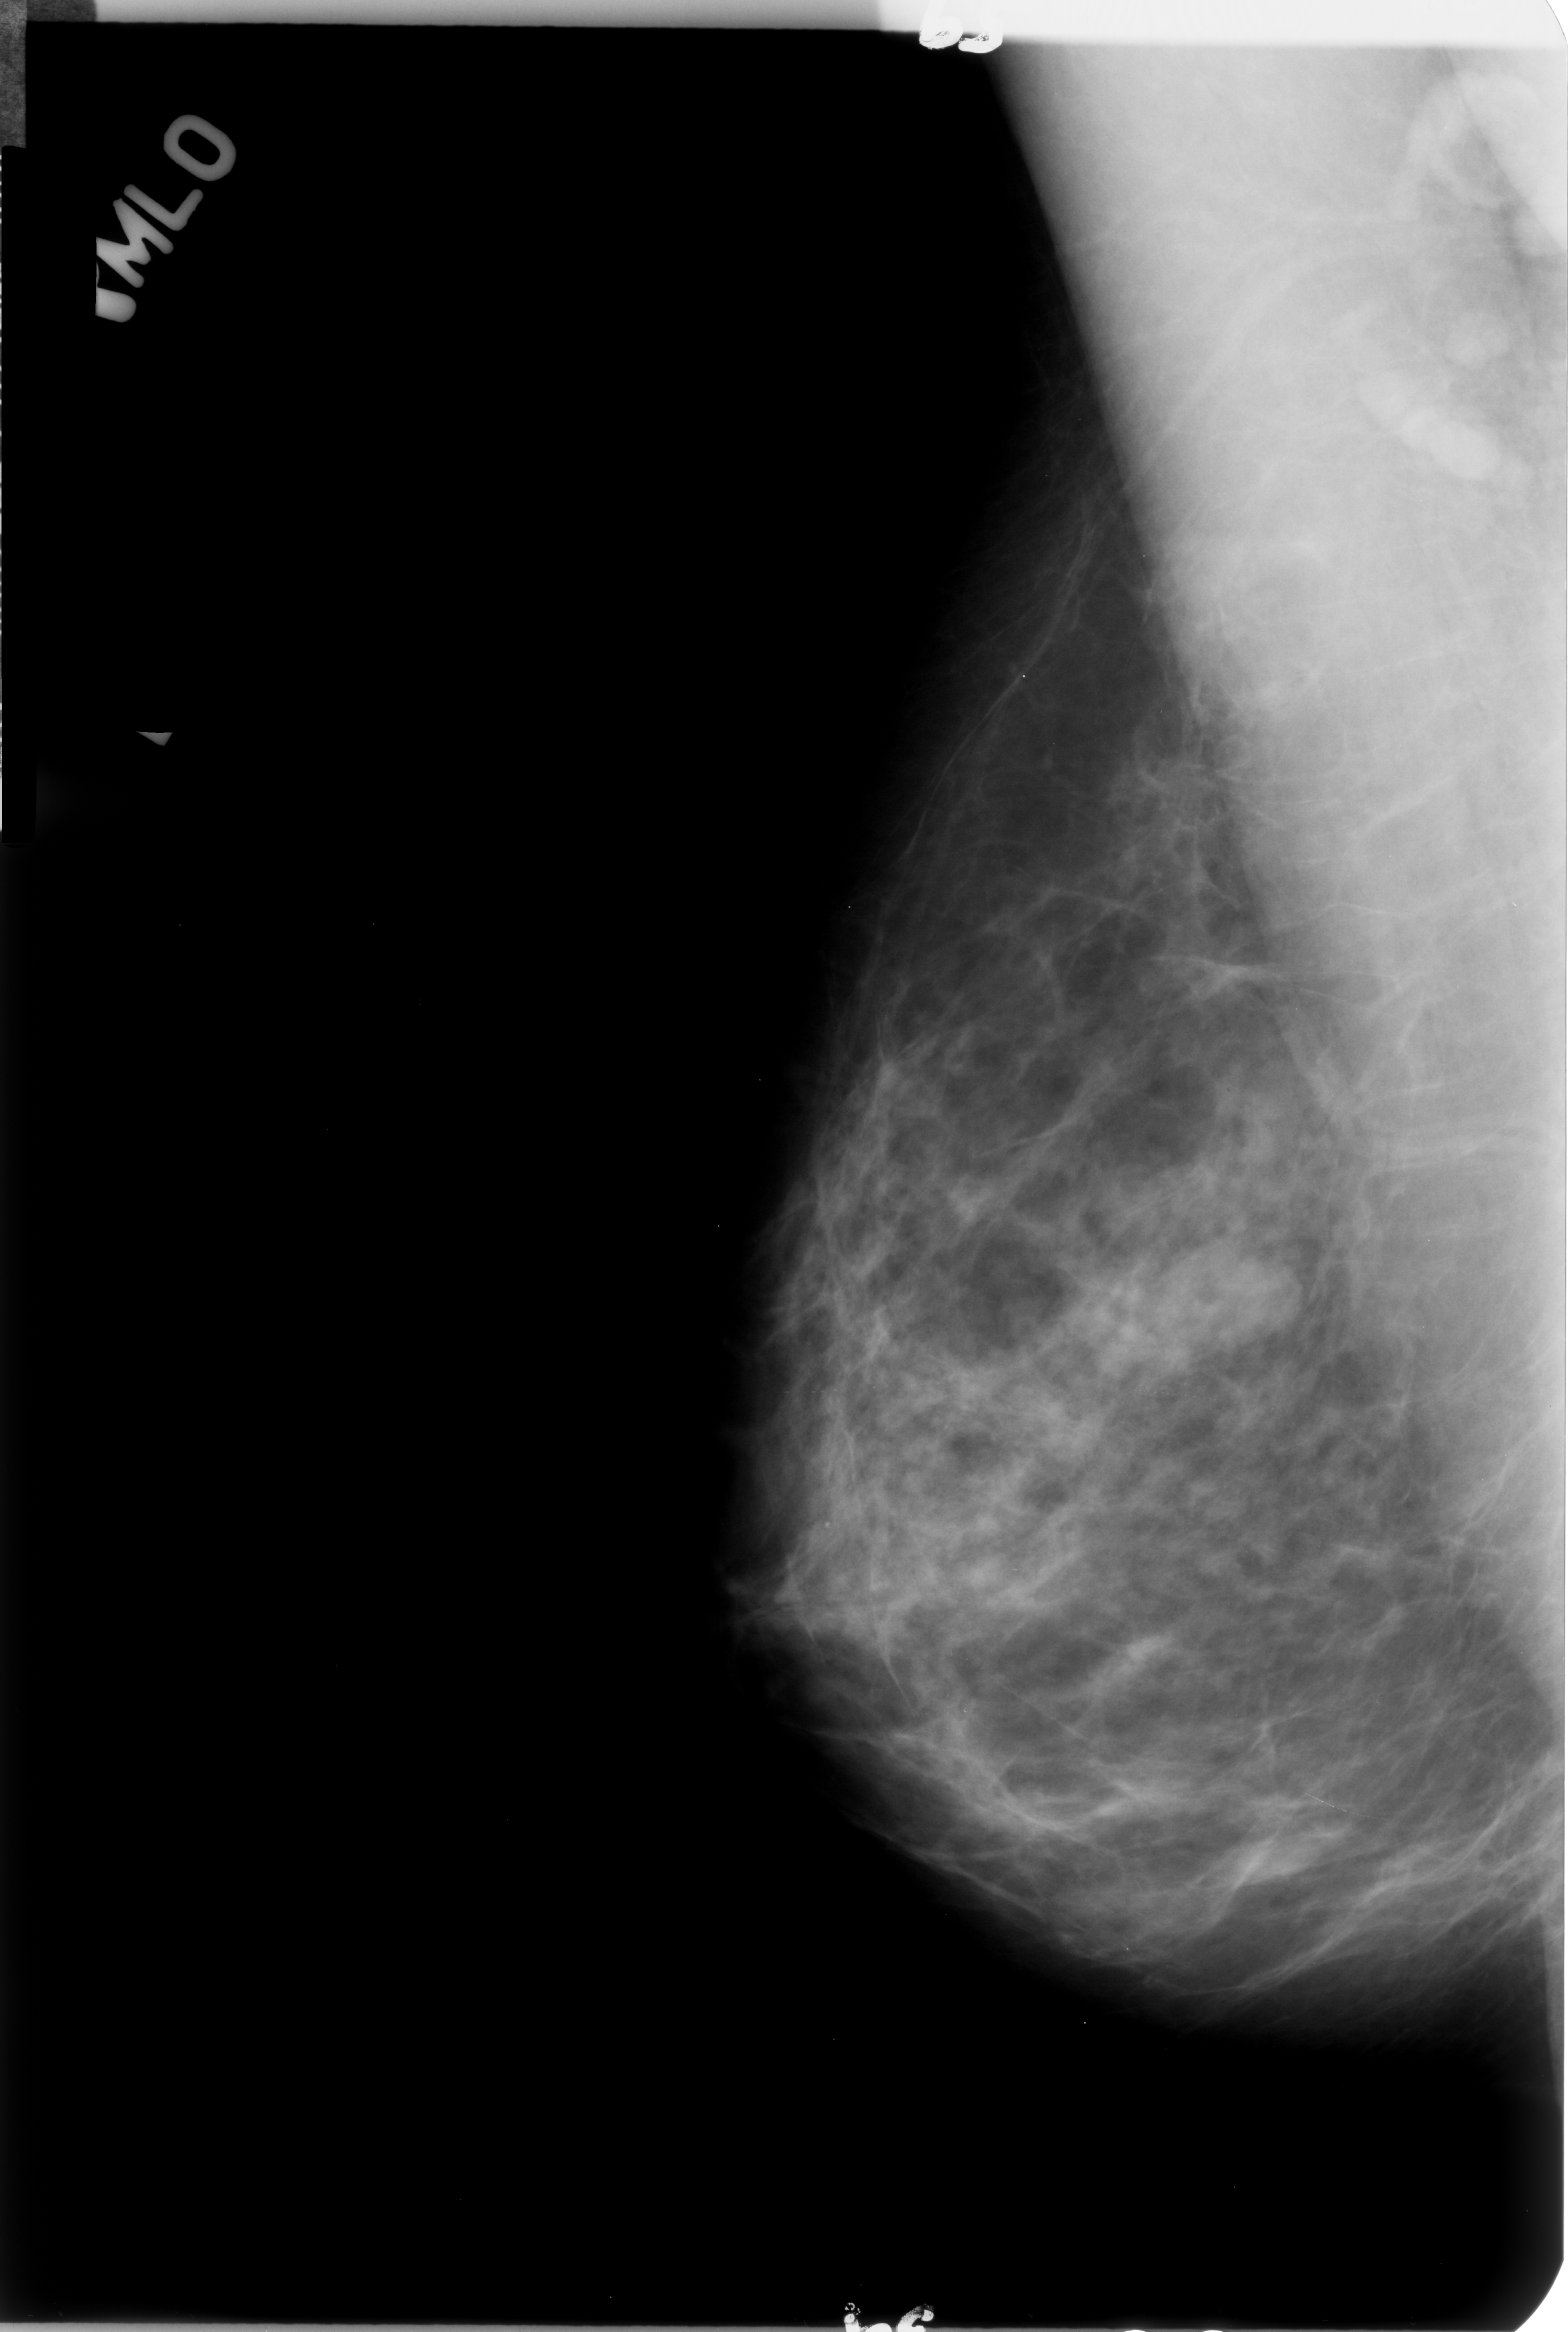
Digitized screen-film mammogram; right breast; mediolateral oblique (MLO) view; BI-RADS breast density category 3 (scale 1–4).
- Marked abnormality: mass, shape oval, margins circumscribed; BI-RADS assessment category 3; subtlety rating 3 on a 1 (subtle) to 5 (obvious) scale; pathology (as recorded): benign.